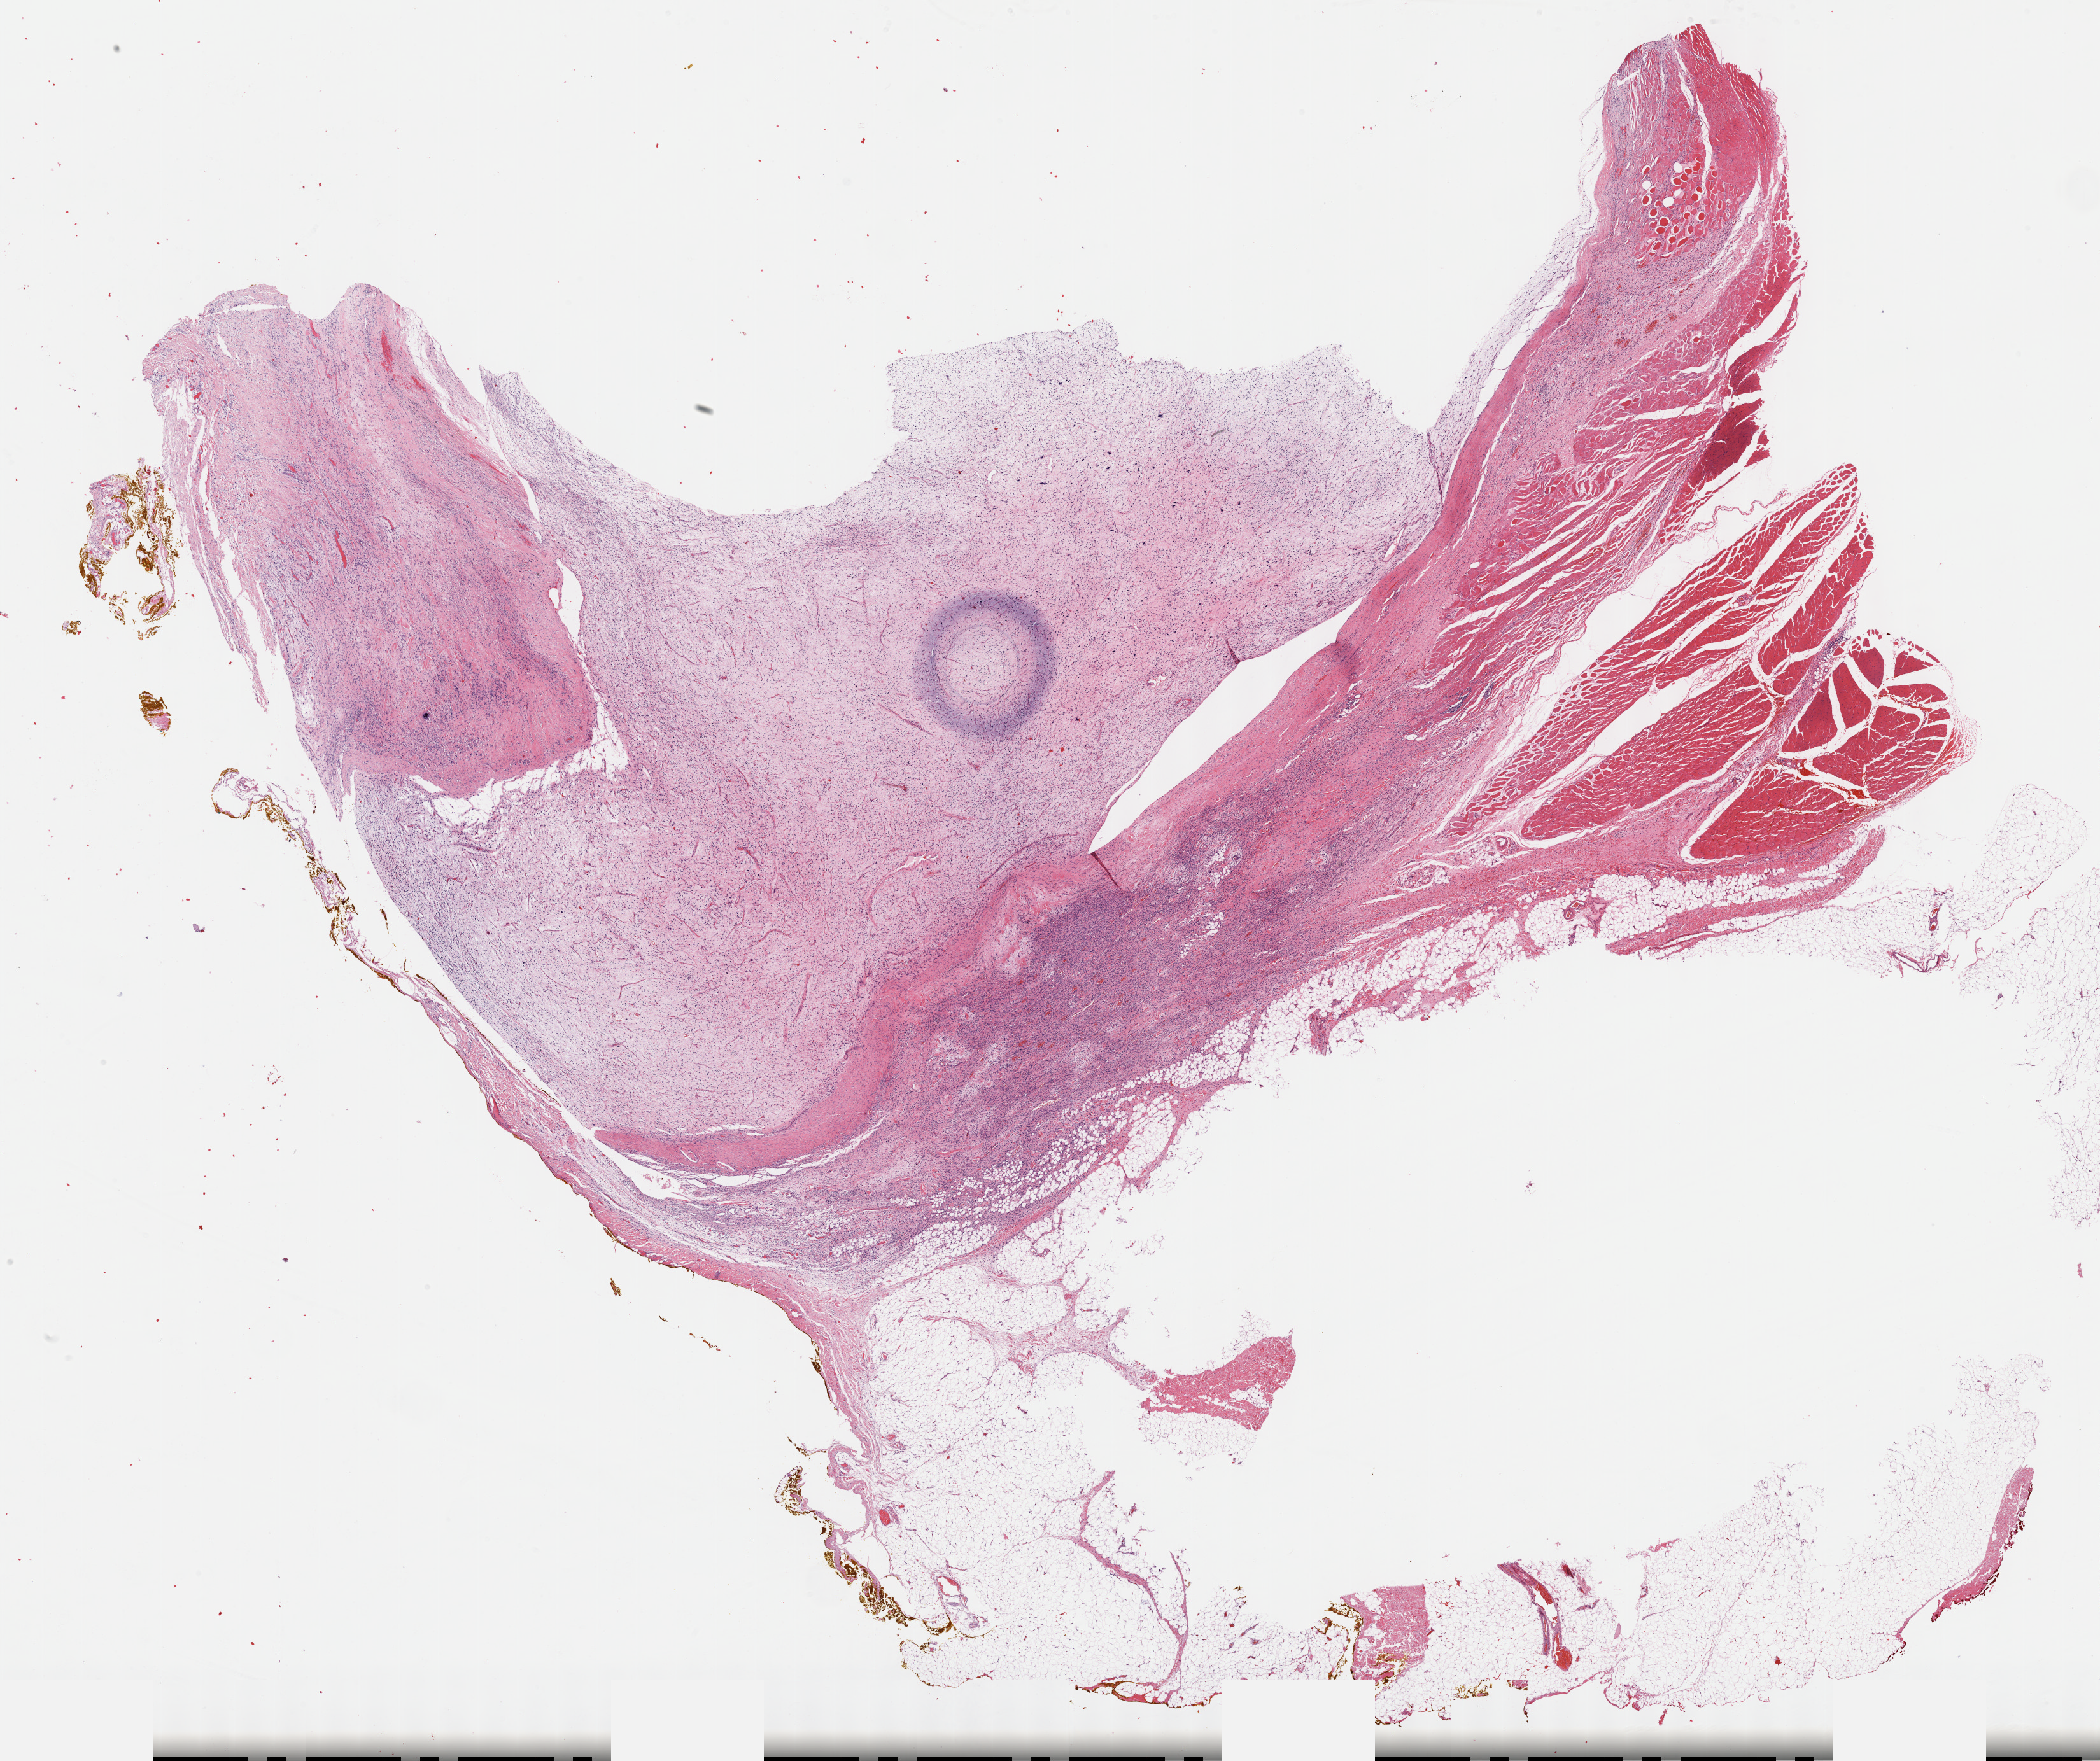
Digitized Hematoxylin and eosin (H&E) stained tissue section (whole slide), low-resolution overview of the scanned area, about 26.7 x 22.4 mm (acquisition: 40x scan); formalin-fixed paraffin-embedded (FFPE) diagnostic section; connective, subcutaneous and other soft tissues, primary tumour sample. Male, age 35 years at initial diagnosis.
Pathologic diagnosis: Fibromyxosarcoma (connective, subcutaneous and other soft tissues of lower limb and hip).